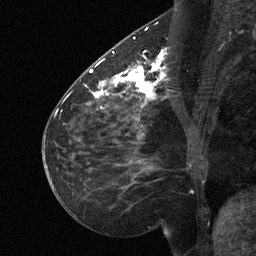
Breast MRI (dynamic contrast-enhanced), one sagittal slice; position 27 of 64 along the scan axis; dynamic contrast-enhanced study with each time point stored as its own series, time point 2 of 3 at this slice position (early post-contrast, ordered by acquisition time); 1.5 T; TE 4.8 ms, TR 27 ms; 256 × 256 image matrix. Female patient, age 51 years. Case-level facts recorded for this patient, not image findings: setting: breast cancer imaged before/during neoadjuvant chemotherapy; receptor status: HR-positive, HER2-negative.
Structures marked on this image (semi-automatic segmentation, software-assisted and operator-edited):
- analysis volume of interest (the breast-tissue region the enhancement analysis was run in; not a lesion): bounding box (x1, y1, x2, y2) in pixels: (112, 46, 169, 106)
- tumour enhancement mask (voxels above the 90 % enhancement threshold inside the analysis volume of interest): (112, 52, 166, 106)